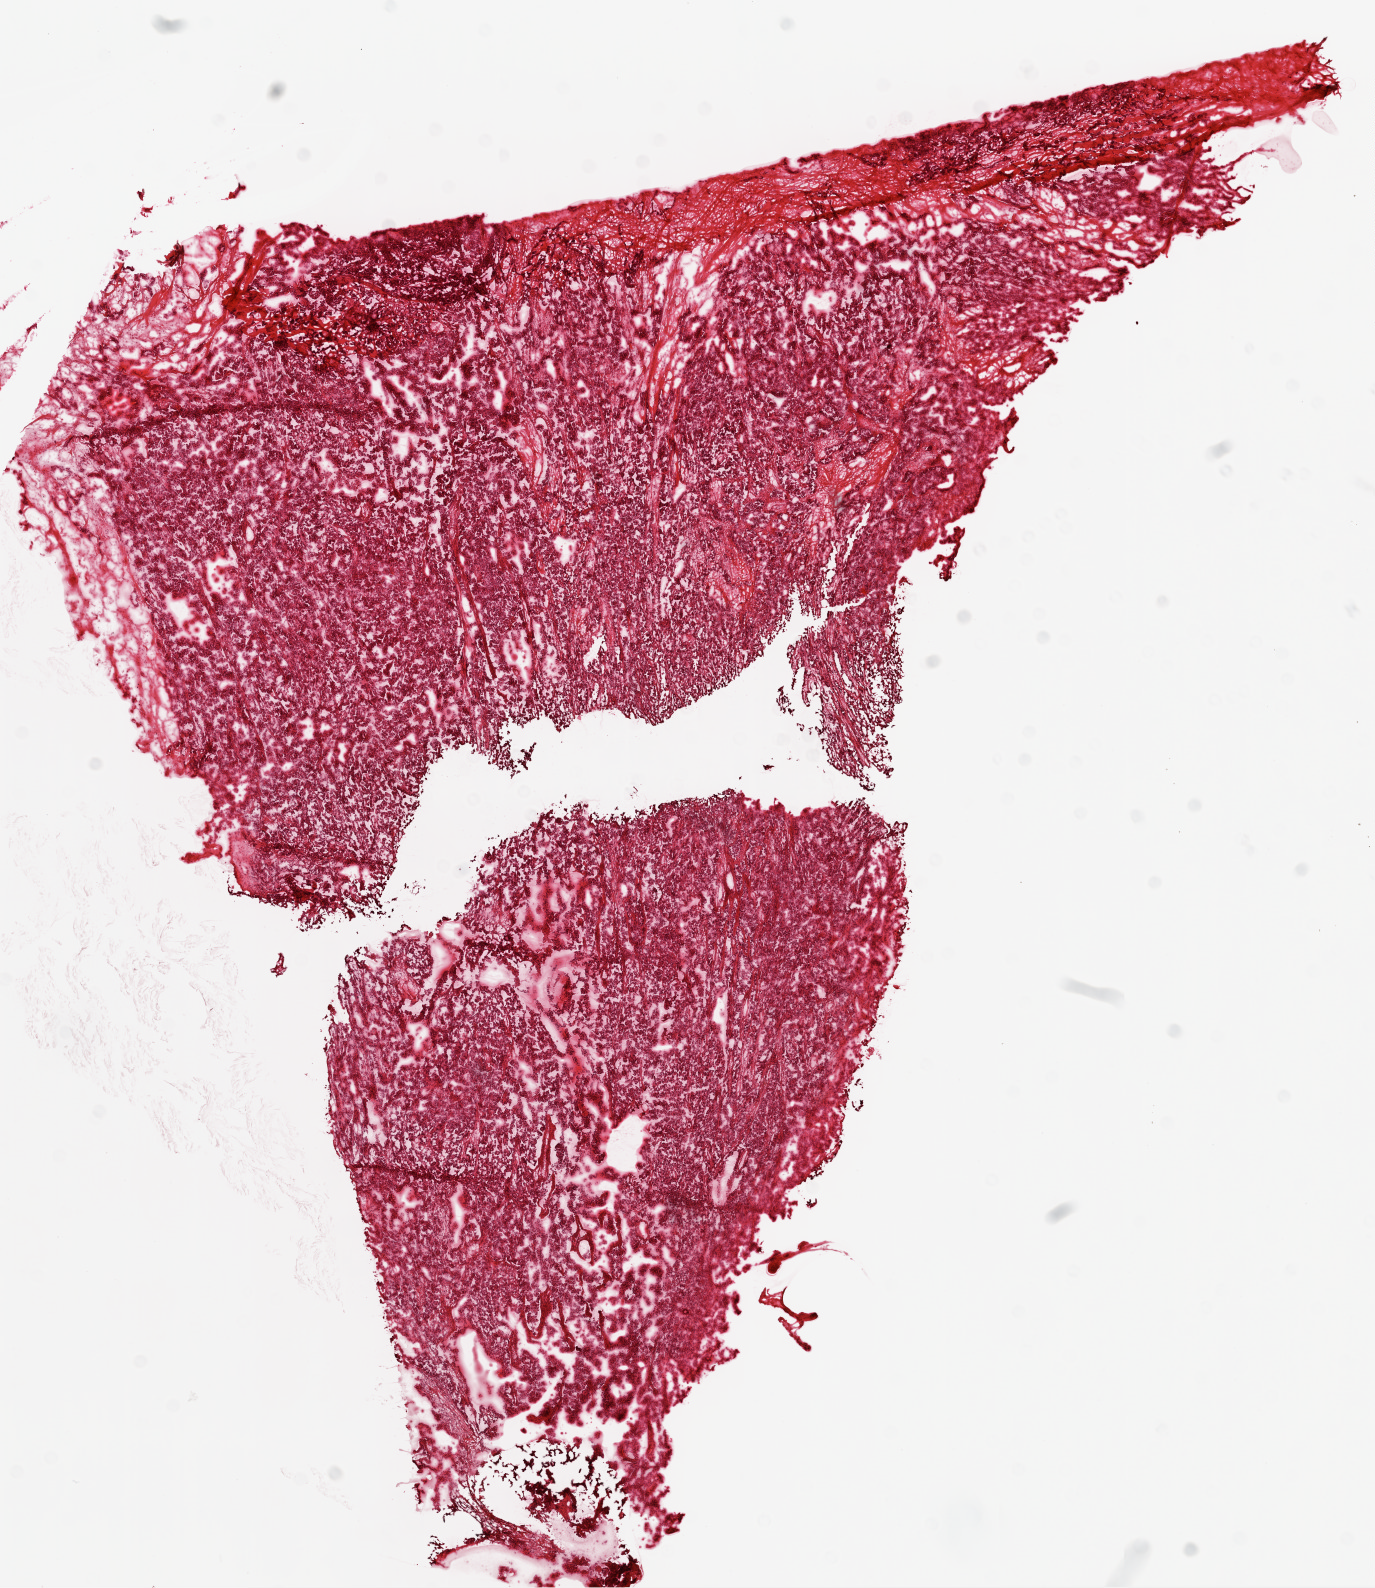
Whole-slide histology image, H&E-stained, shown as a low-resolution overview of the whole scanned area (about 11.0 x 12.7 mm); frozen section from the top of the tissue portion; sample: primary tumour, ovary. Patient: female, age at initial diagnosis 70 years. Histologic grade: G3 (poorly differentiated). Composition of this section per pathologist review: tumour cells 90%, tumour nuclei 90%, normal cells 0%, stromal cells 9%, necrosis 1%.
Laterality: left. FIGO stage: IIIC. Pathologic diagnosis: Serous cystadenocarcinoma, NOS.